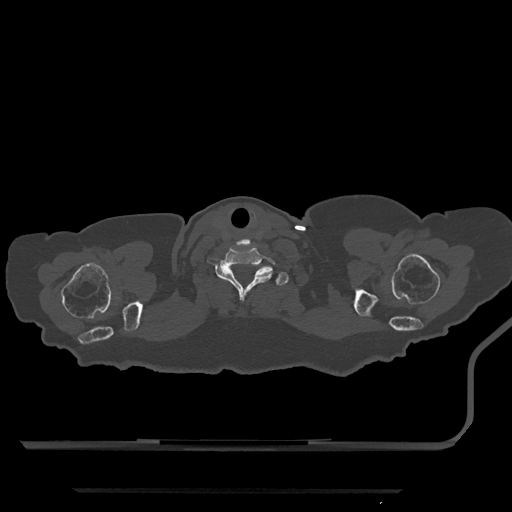
CT including the spine, one axial slice; position 734 of 797 along the scan axis; 120 kVp; bone window (W 1800 / L 400 HU); 0.5 mm slice thickness; 512 × 512 image matrix, field of view 440 × 440 mm. Female patient, age 51 years. From the clinical record (not read from this slice): primary cancer: neuro.
Annotated regions visible in this slice (semi-automatically segmented with operator editing):
- T1 vertebra: bounding box (x1, y1, x2, y2) in pixels: (229, 268, 289, 286)